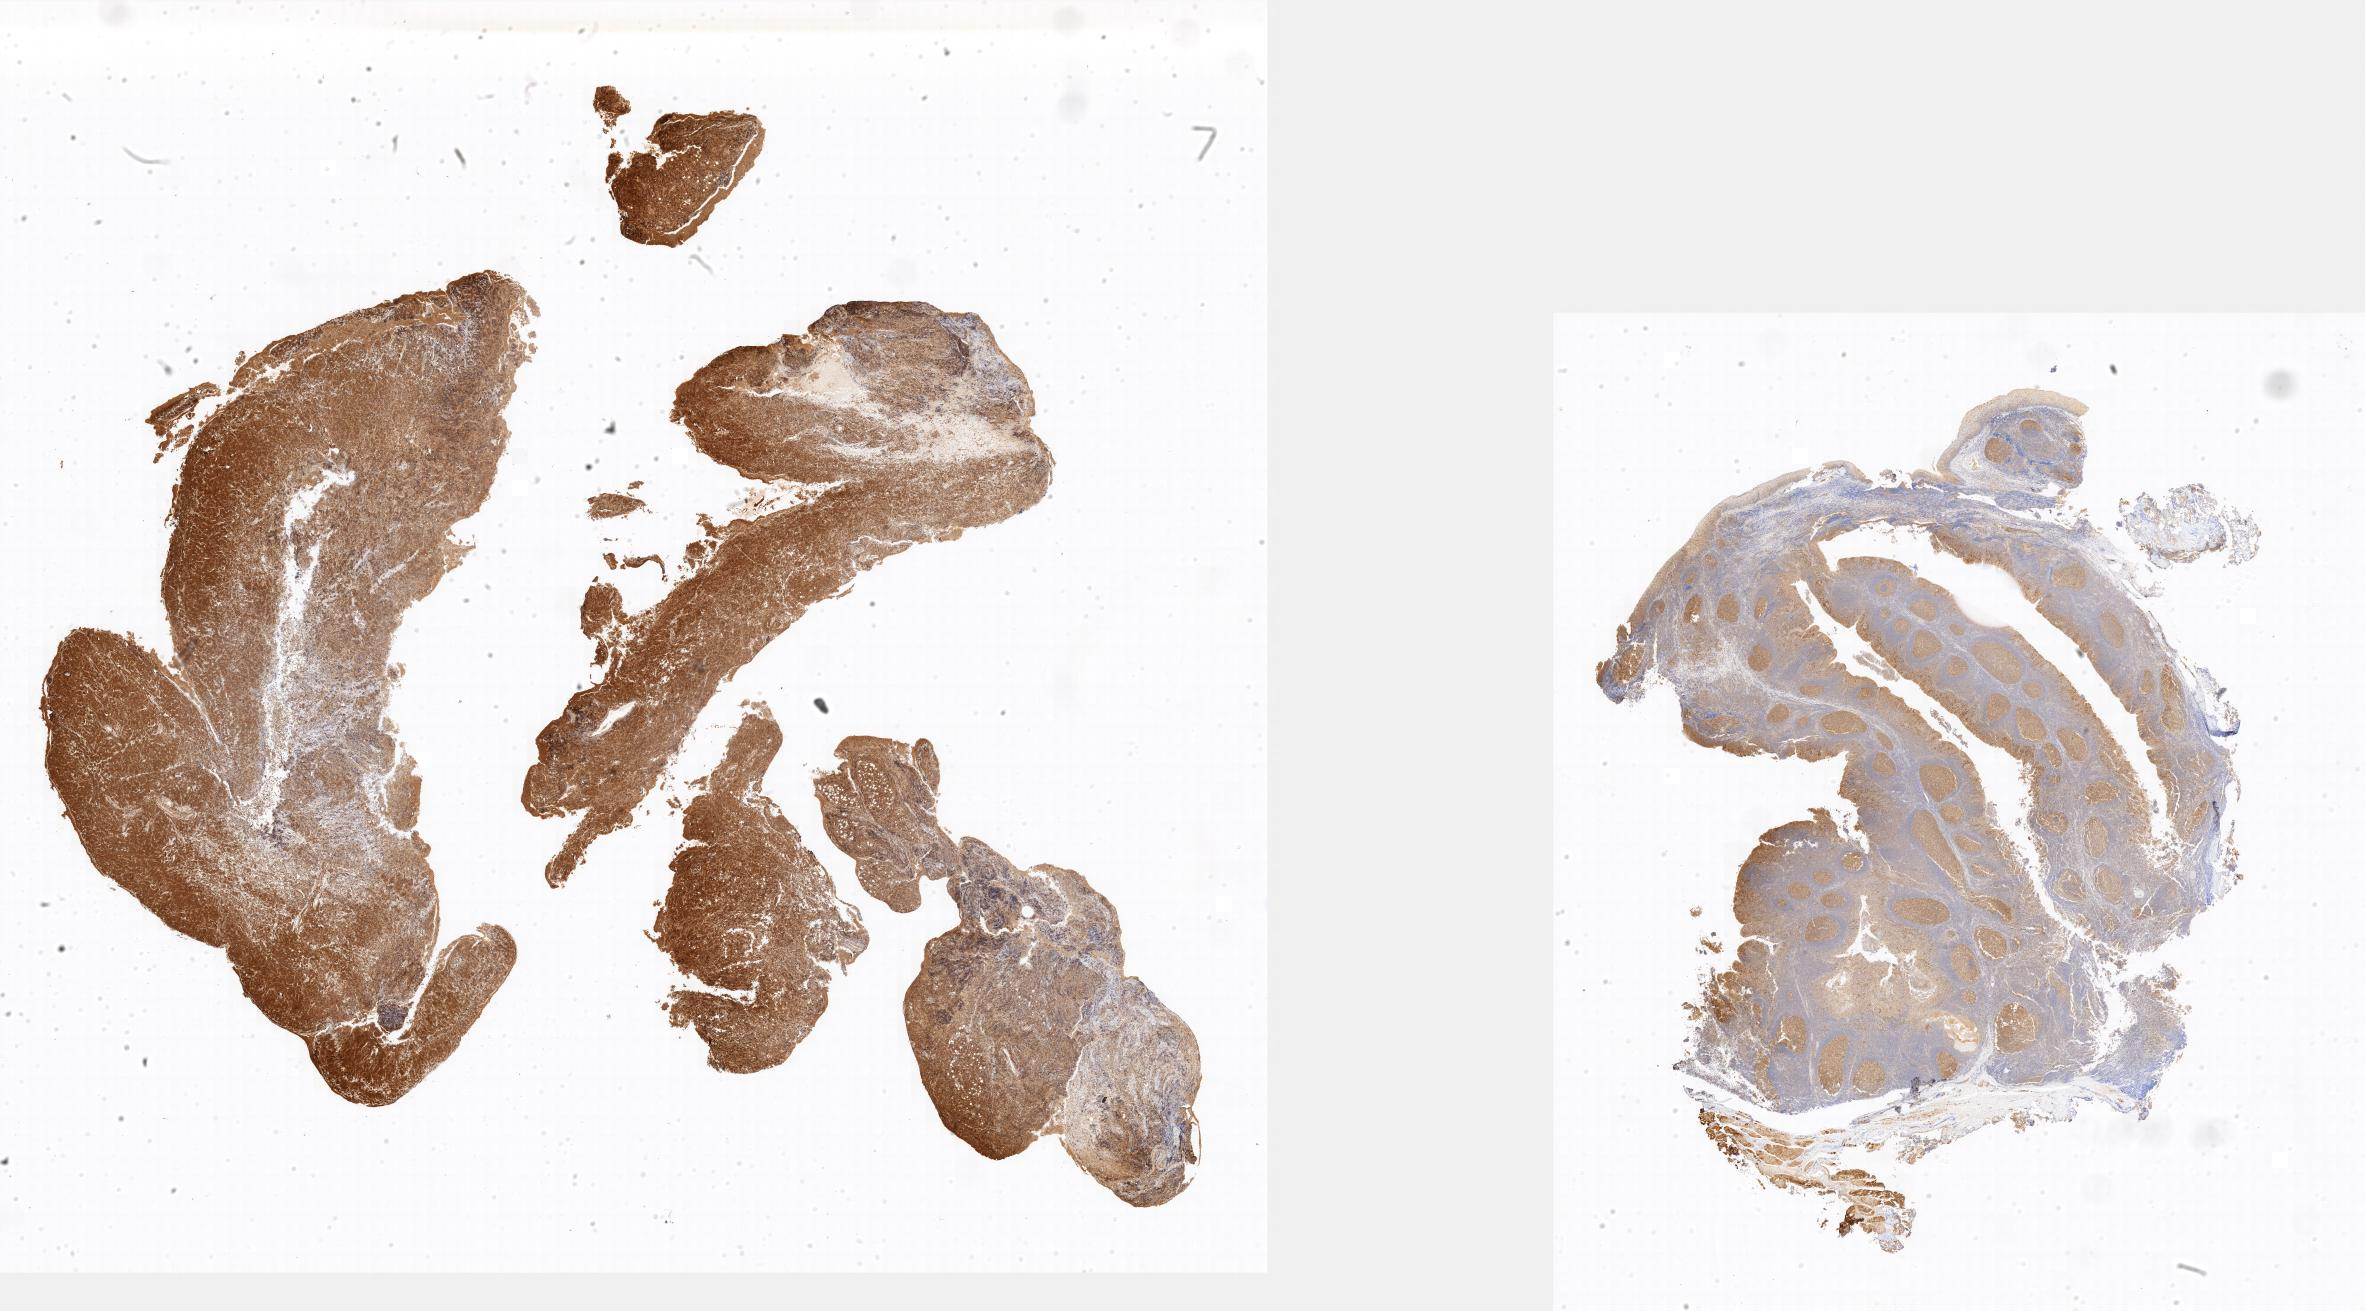
Whole-slide image, immunohistochemical stain for BCL6 — whole scanned area shown as a low-resolution overview; tumor tissue; anatomic site: abdomen proper. Male, age 5 years at initial diagnosis.
Diagnosis: Burkitt lymphoma, NOS.